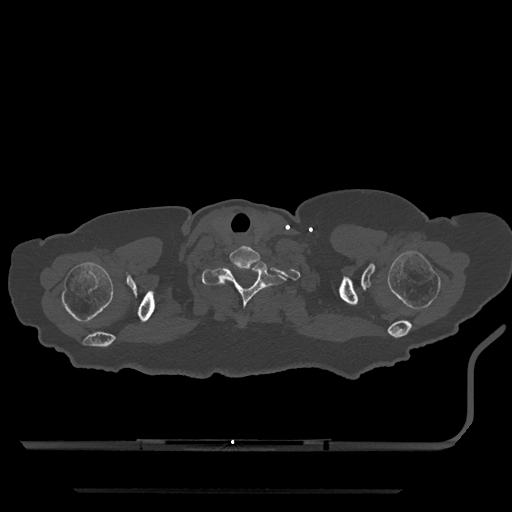
CT including the spine, one axial slice. Slice 718 of 797 in the series (ordered by position). Reconstruction kernel Br40s/3. Bone window (W 1800 / L 400 HU). 0.5 mm slice thickness. 512 × 512 image matrix. Female patient, age 51 years. Case-level facts recorded for this patient, not image findings: primary cancer: neuro; vertebrae with lytic lesions (as recorded): T8.
Annotated regions visible in this slice (semi-automatically segmented with operator editing):
- T1 vertebra: bounding box <202,262,287,309> (left, top, right, bottom; pixels)